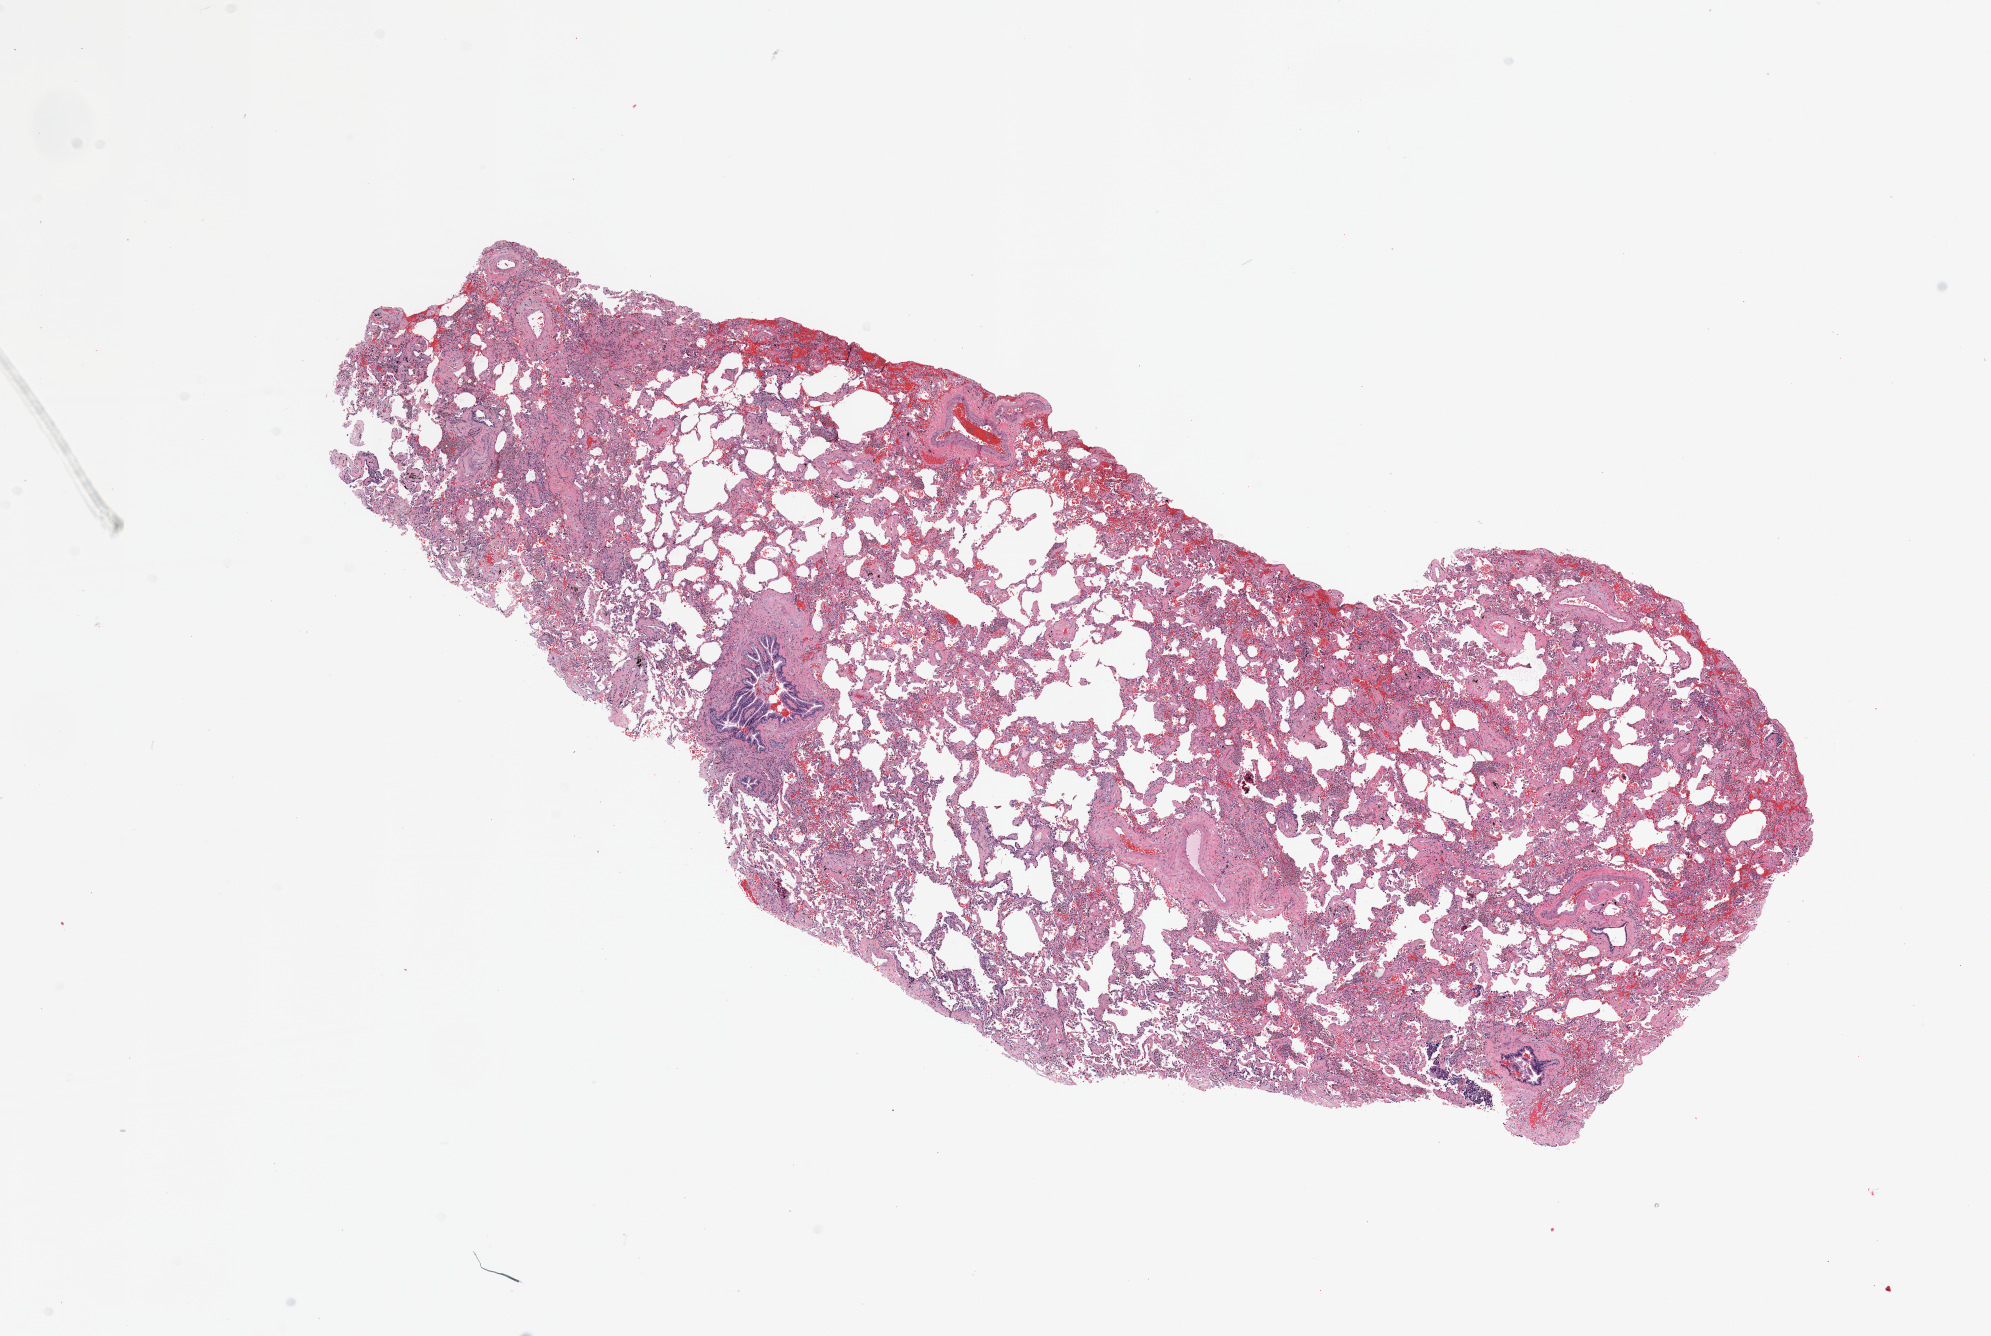
Whole-slide histology image, H&E, low-resolution overview of the scanned area, about 15.8 x 10.6 mm (acquisition: 20x scan), normal (non-tumour) tissue sample, lung. Female, 62 y/o.
This section: normal (non-tumour) tissue from the same patient. Patient diagnosis: Adenocarcinoma, NOS.